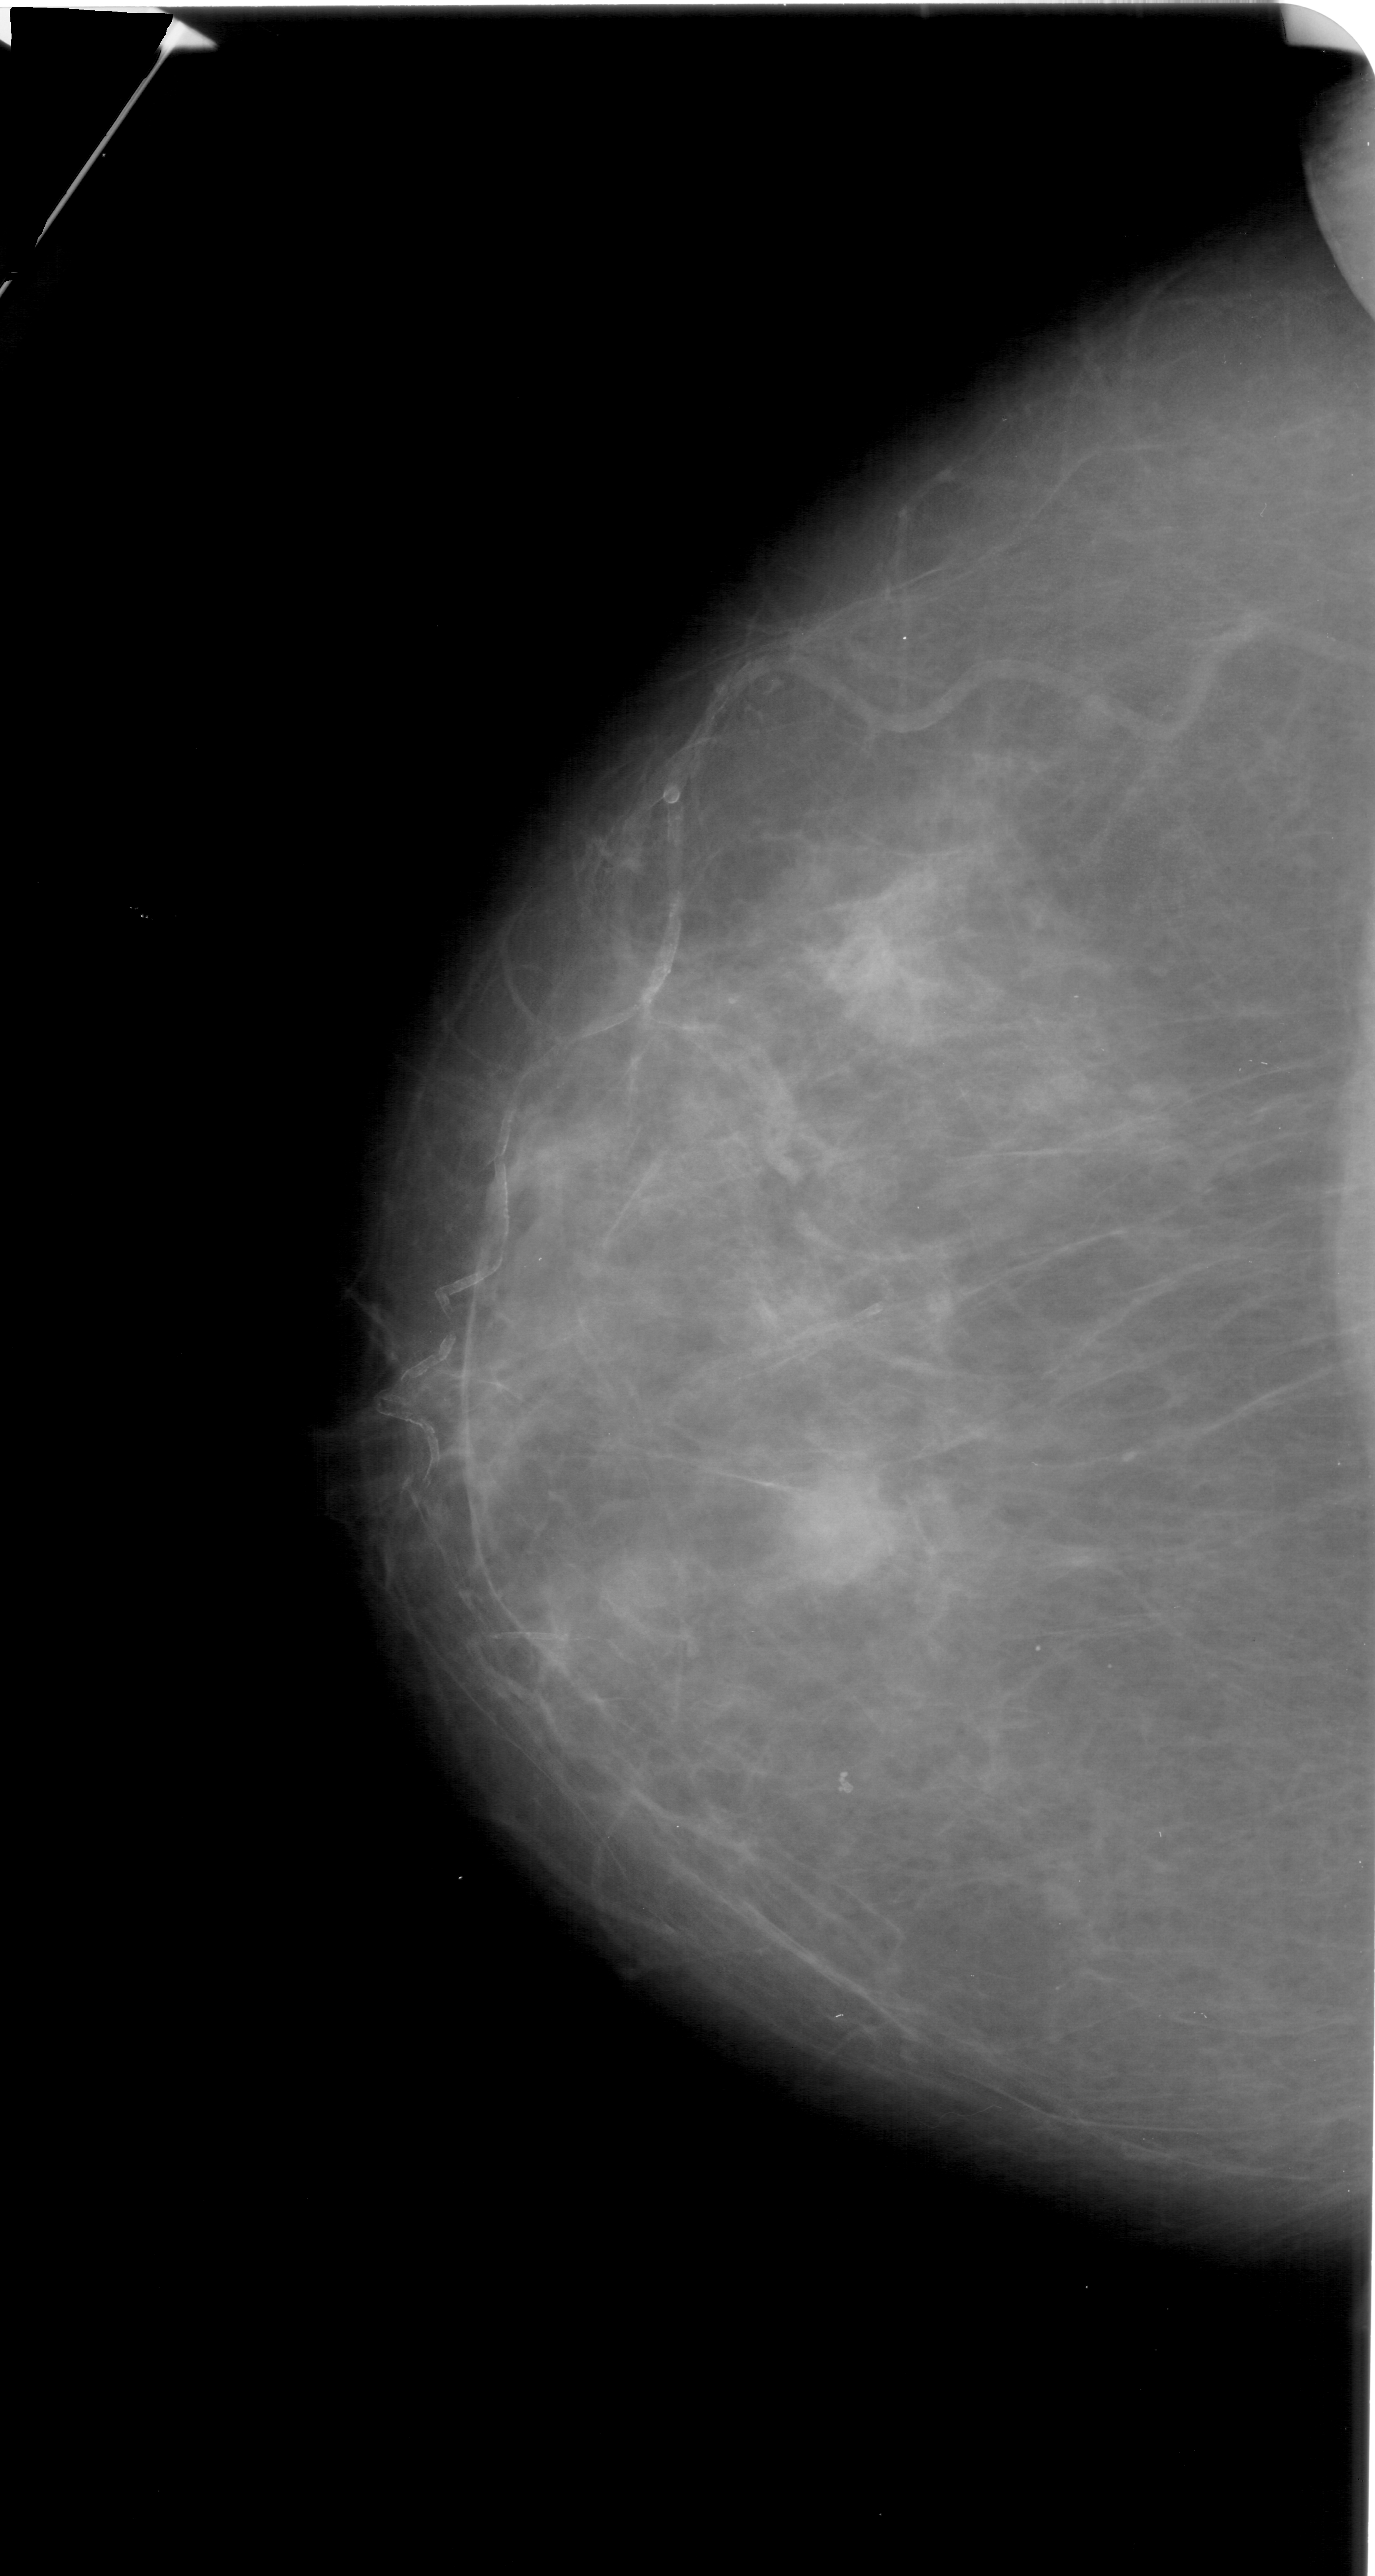
Digitized screen-film mammogram; left breast; craniocaudal (CC) view; BI-RADS breast density category 3 (scale 1–4); 1375 × 2576 image matrix.
Marked abnormalities (boxes around the expert regions of interest):
- mass, shape round, margins ill defined; BI-RADS assessment category 4; subtlety rating 3 on a 1 (subtle) to 5 (obvious) scale; pathology (as recorded): malignant: box from (x=768, y=1473) to (x=873, y=1577) px